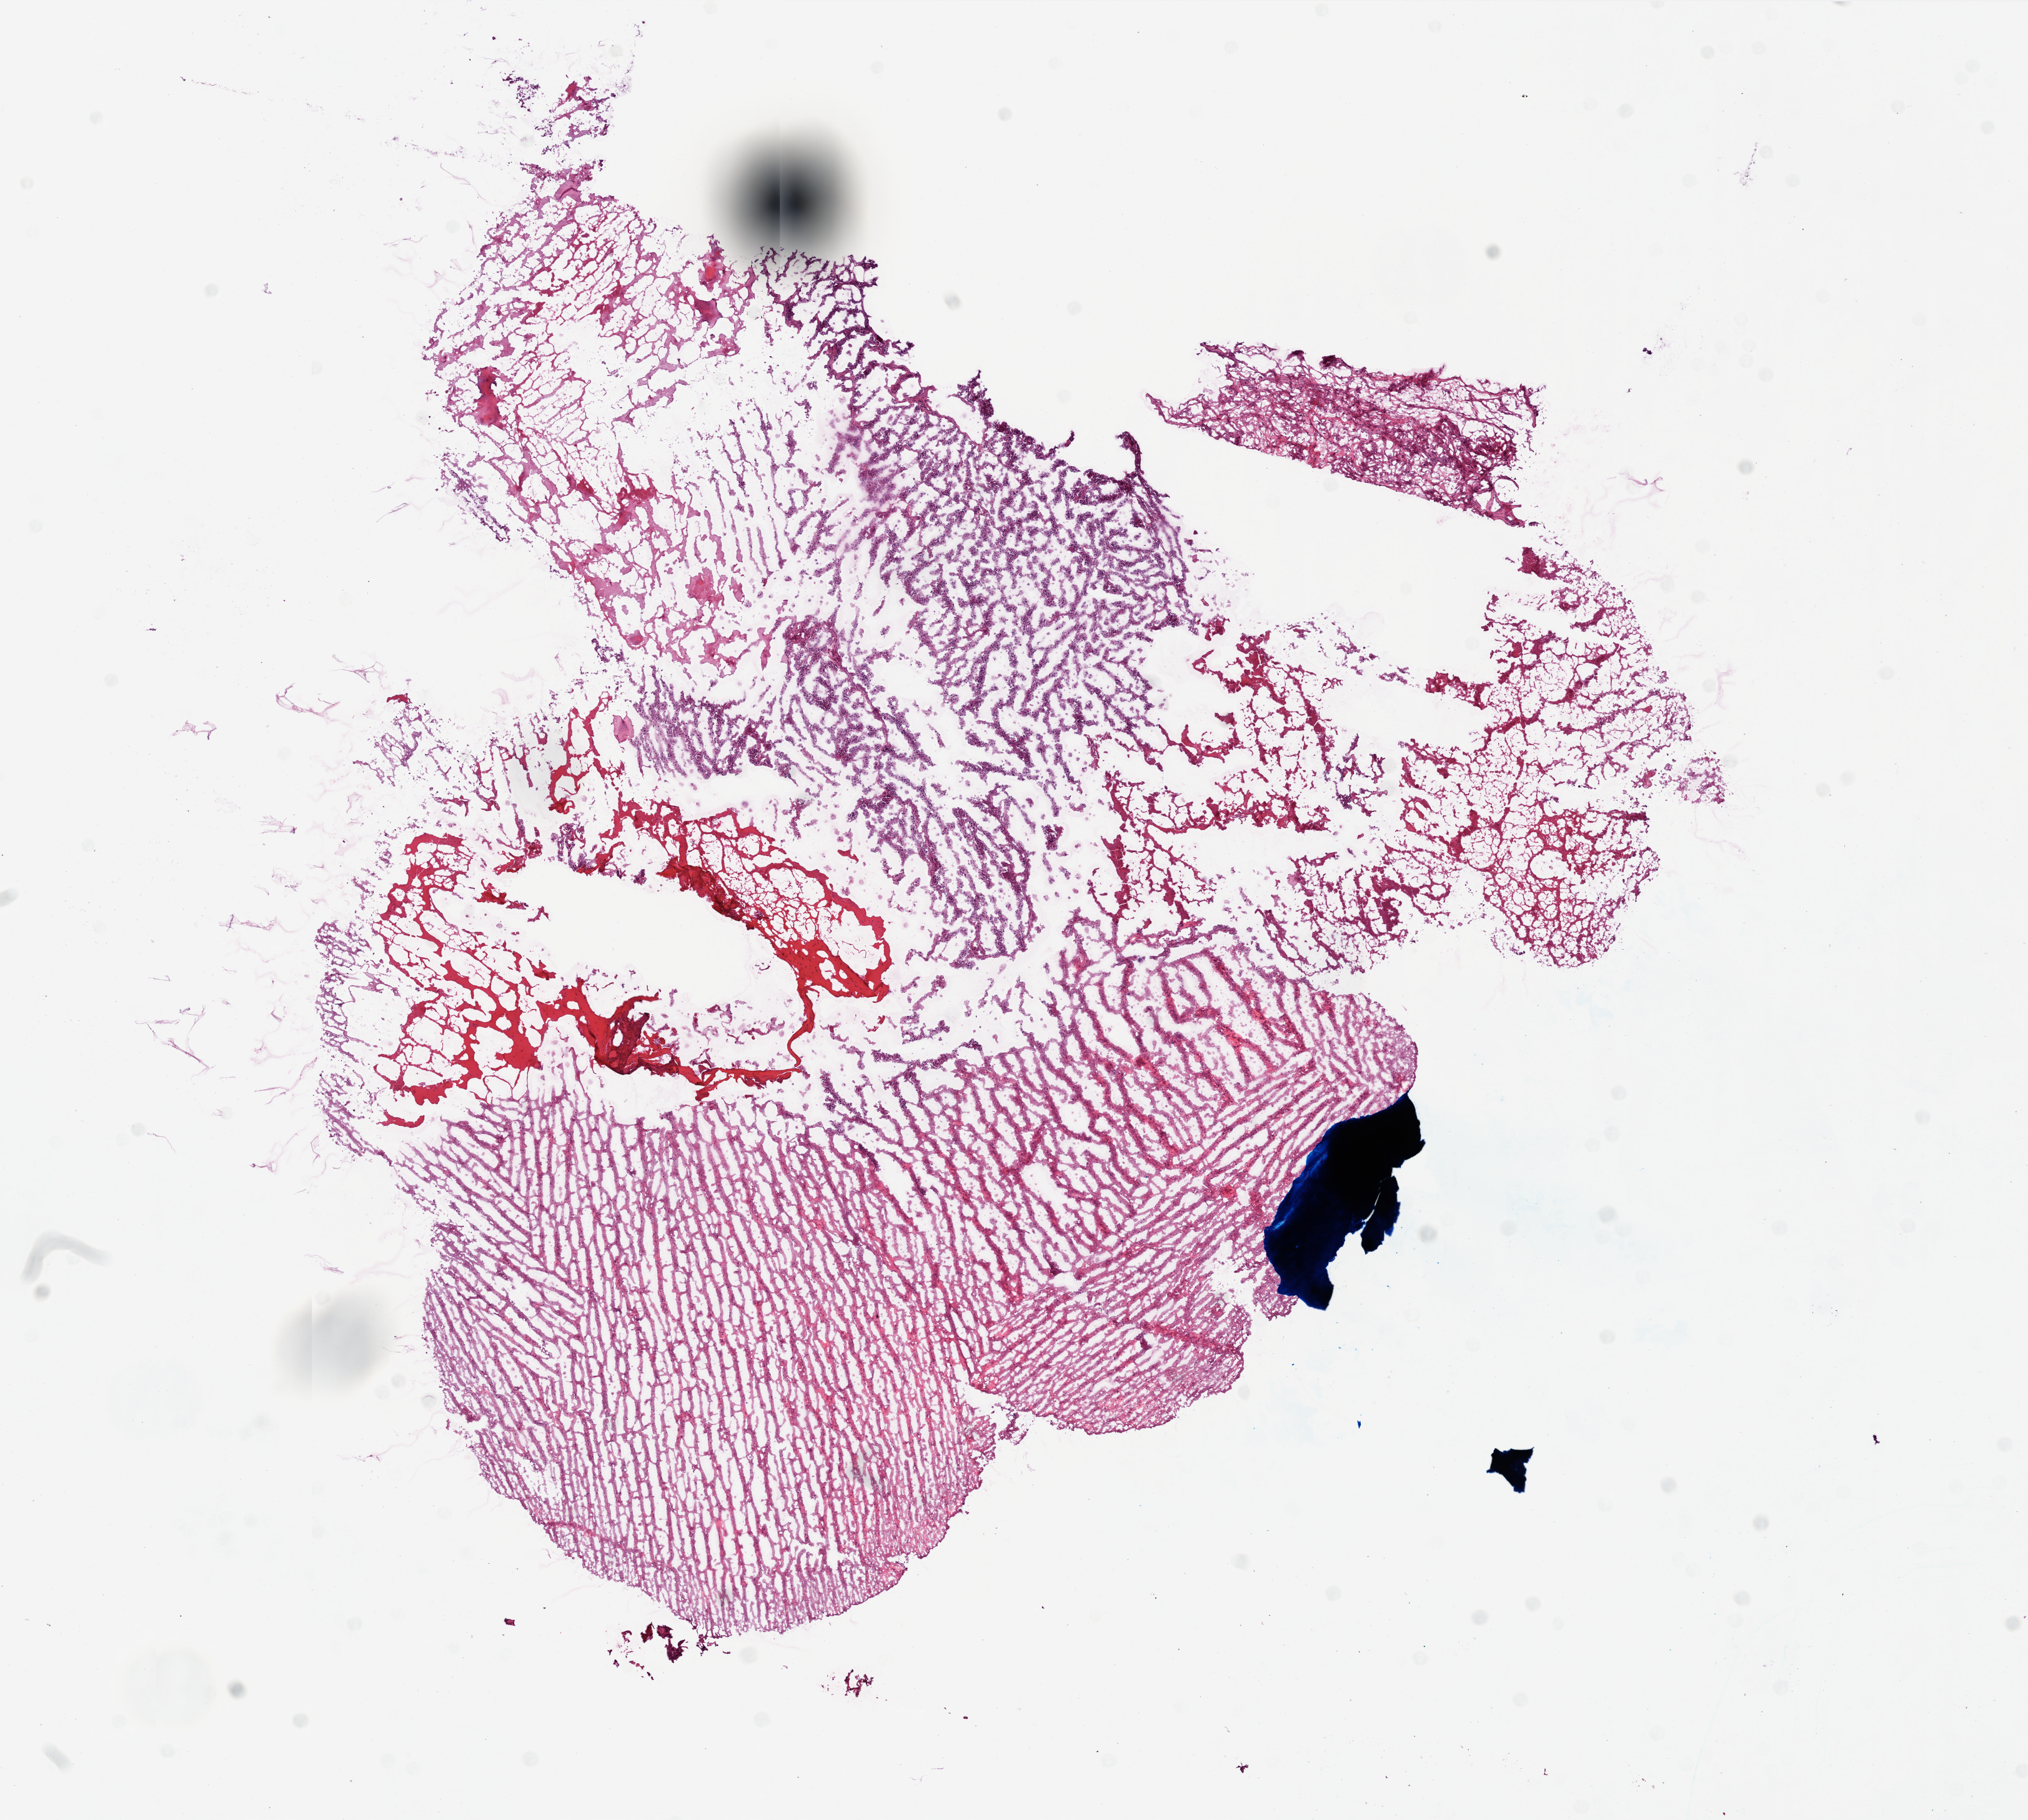
Digitized H&E tissue section (whole slide) — low-resolution overview of the scanned area, about 13.0 x 11.7 mm (from a 20x scan); frozen section; primary tumour sample from the brain. Patient: female, age at initial diagnosis 46 years. Composition of this section per pathologist review: tumour cells 25%, tumour nuclei 100%, normal cells 50%, necrosis 25%.
* histologic diagnosis: Glioblastoma